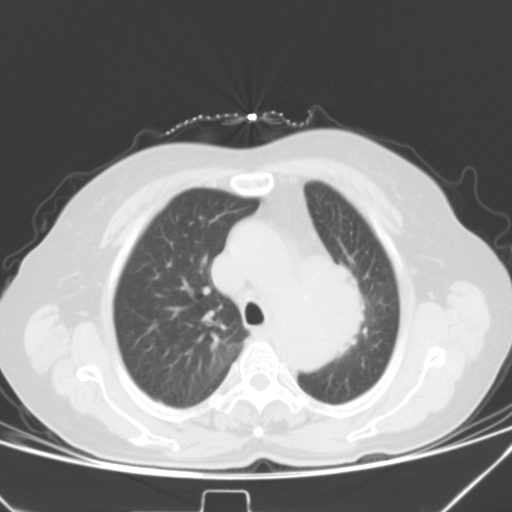
Chest CT, one axial slice; position 32 of 42 along the scan axis; lung window (W 1500 / L -600 HU); 5 mm slice thickness; 512 × 512 image matrix, field of view 331 × 331 mm. Female patient, age 59 years. From the clinical record (not read from this slice): clinical TNM (as recorded): T3 N1 M0.
Outlined on this slice (rectangle marked by the reading radiologist):
- lung tumour (recorded histology: small cell carcinoma): bounding box <334,254,372,365> (left, top, right, bottom; pixels)